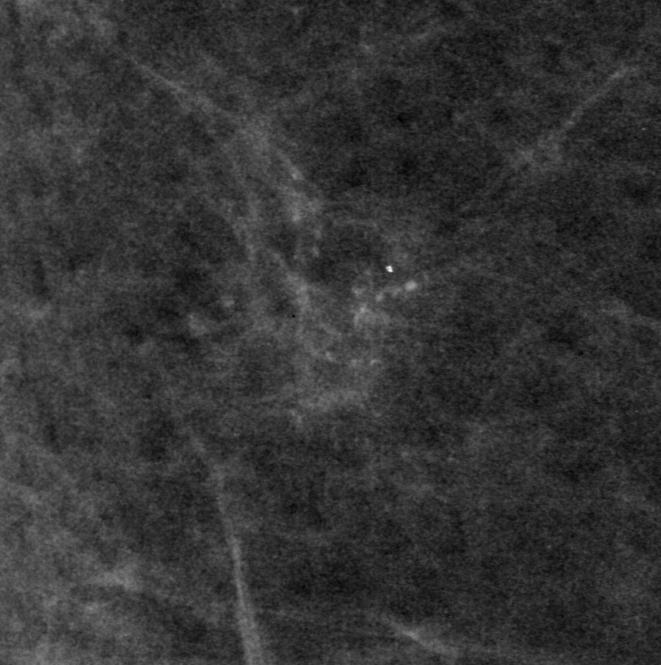
Region of interest cut from a scanned film mammogram (one marked finding), left breast, MLO view.
Marked abnormality: calcifications, morphology fine linear branching, distribution clustered; BI-RADS assessment category 0 (incomplete: needs additional imaging); subtlety rating 4 on a 1 (subtle) to 5 (obvious) scale; pathology result (as recorded, not read from the image): malignant.